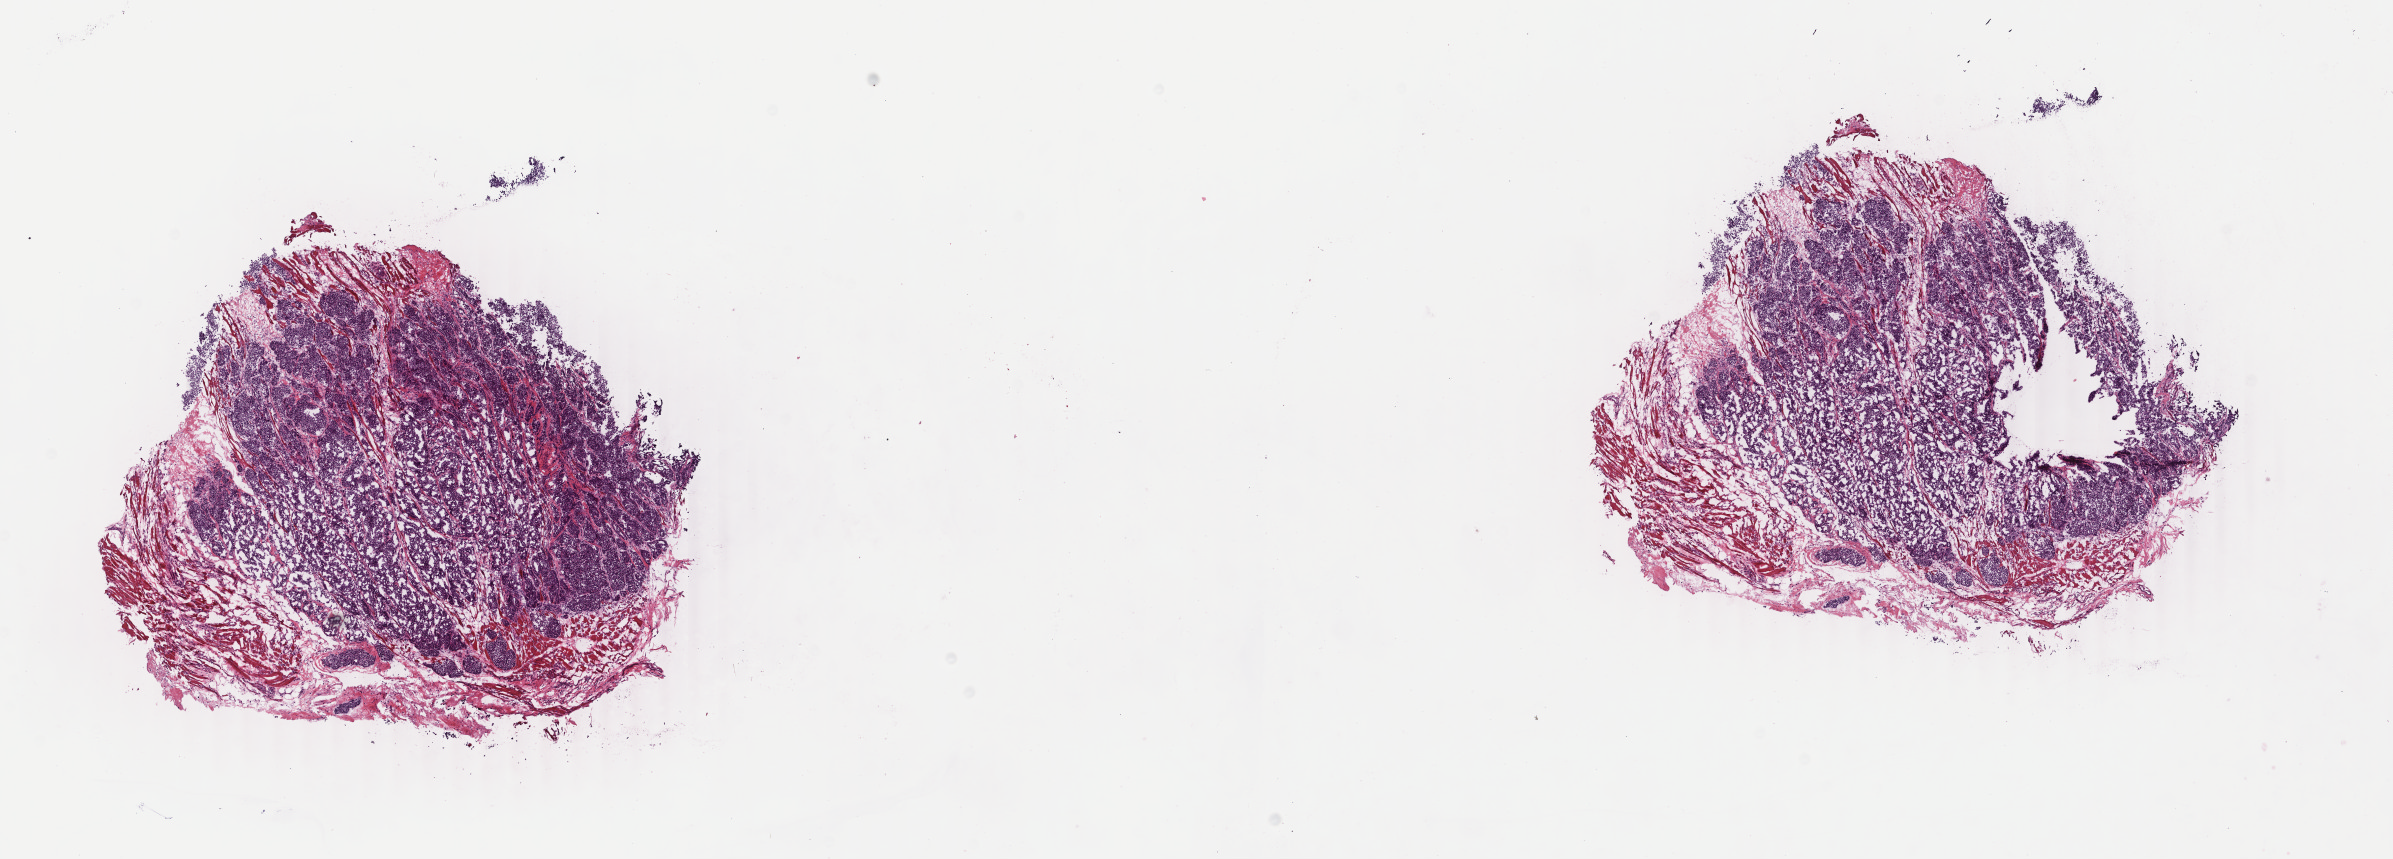
Whole-slide histology image, H&E-stained — whole scanned area (about 19.0 x 6.8 mm, slide scanned at 40x) shown as a low-resolution overview. Frozen section. Sample: primary tumour, breast. Patient: female, age at initial diagnosis 57 years. Composition of this section per pathologist review: tumour cells 82%, tumour nuclei 85%, normal cells 0%, stromal cells 18%, necrosis 0%. Infiltration values recorded for this section: lymphocyte infiltration 1%, monocyte infiltration 0%, neutrophil infiltration 0%.
Pathologic diagnosis: Infiltrating duct carcinoma, NOS. Laterality: left.